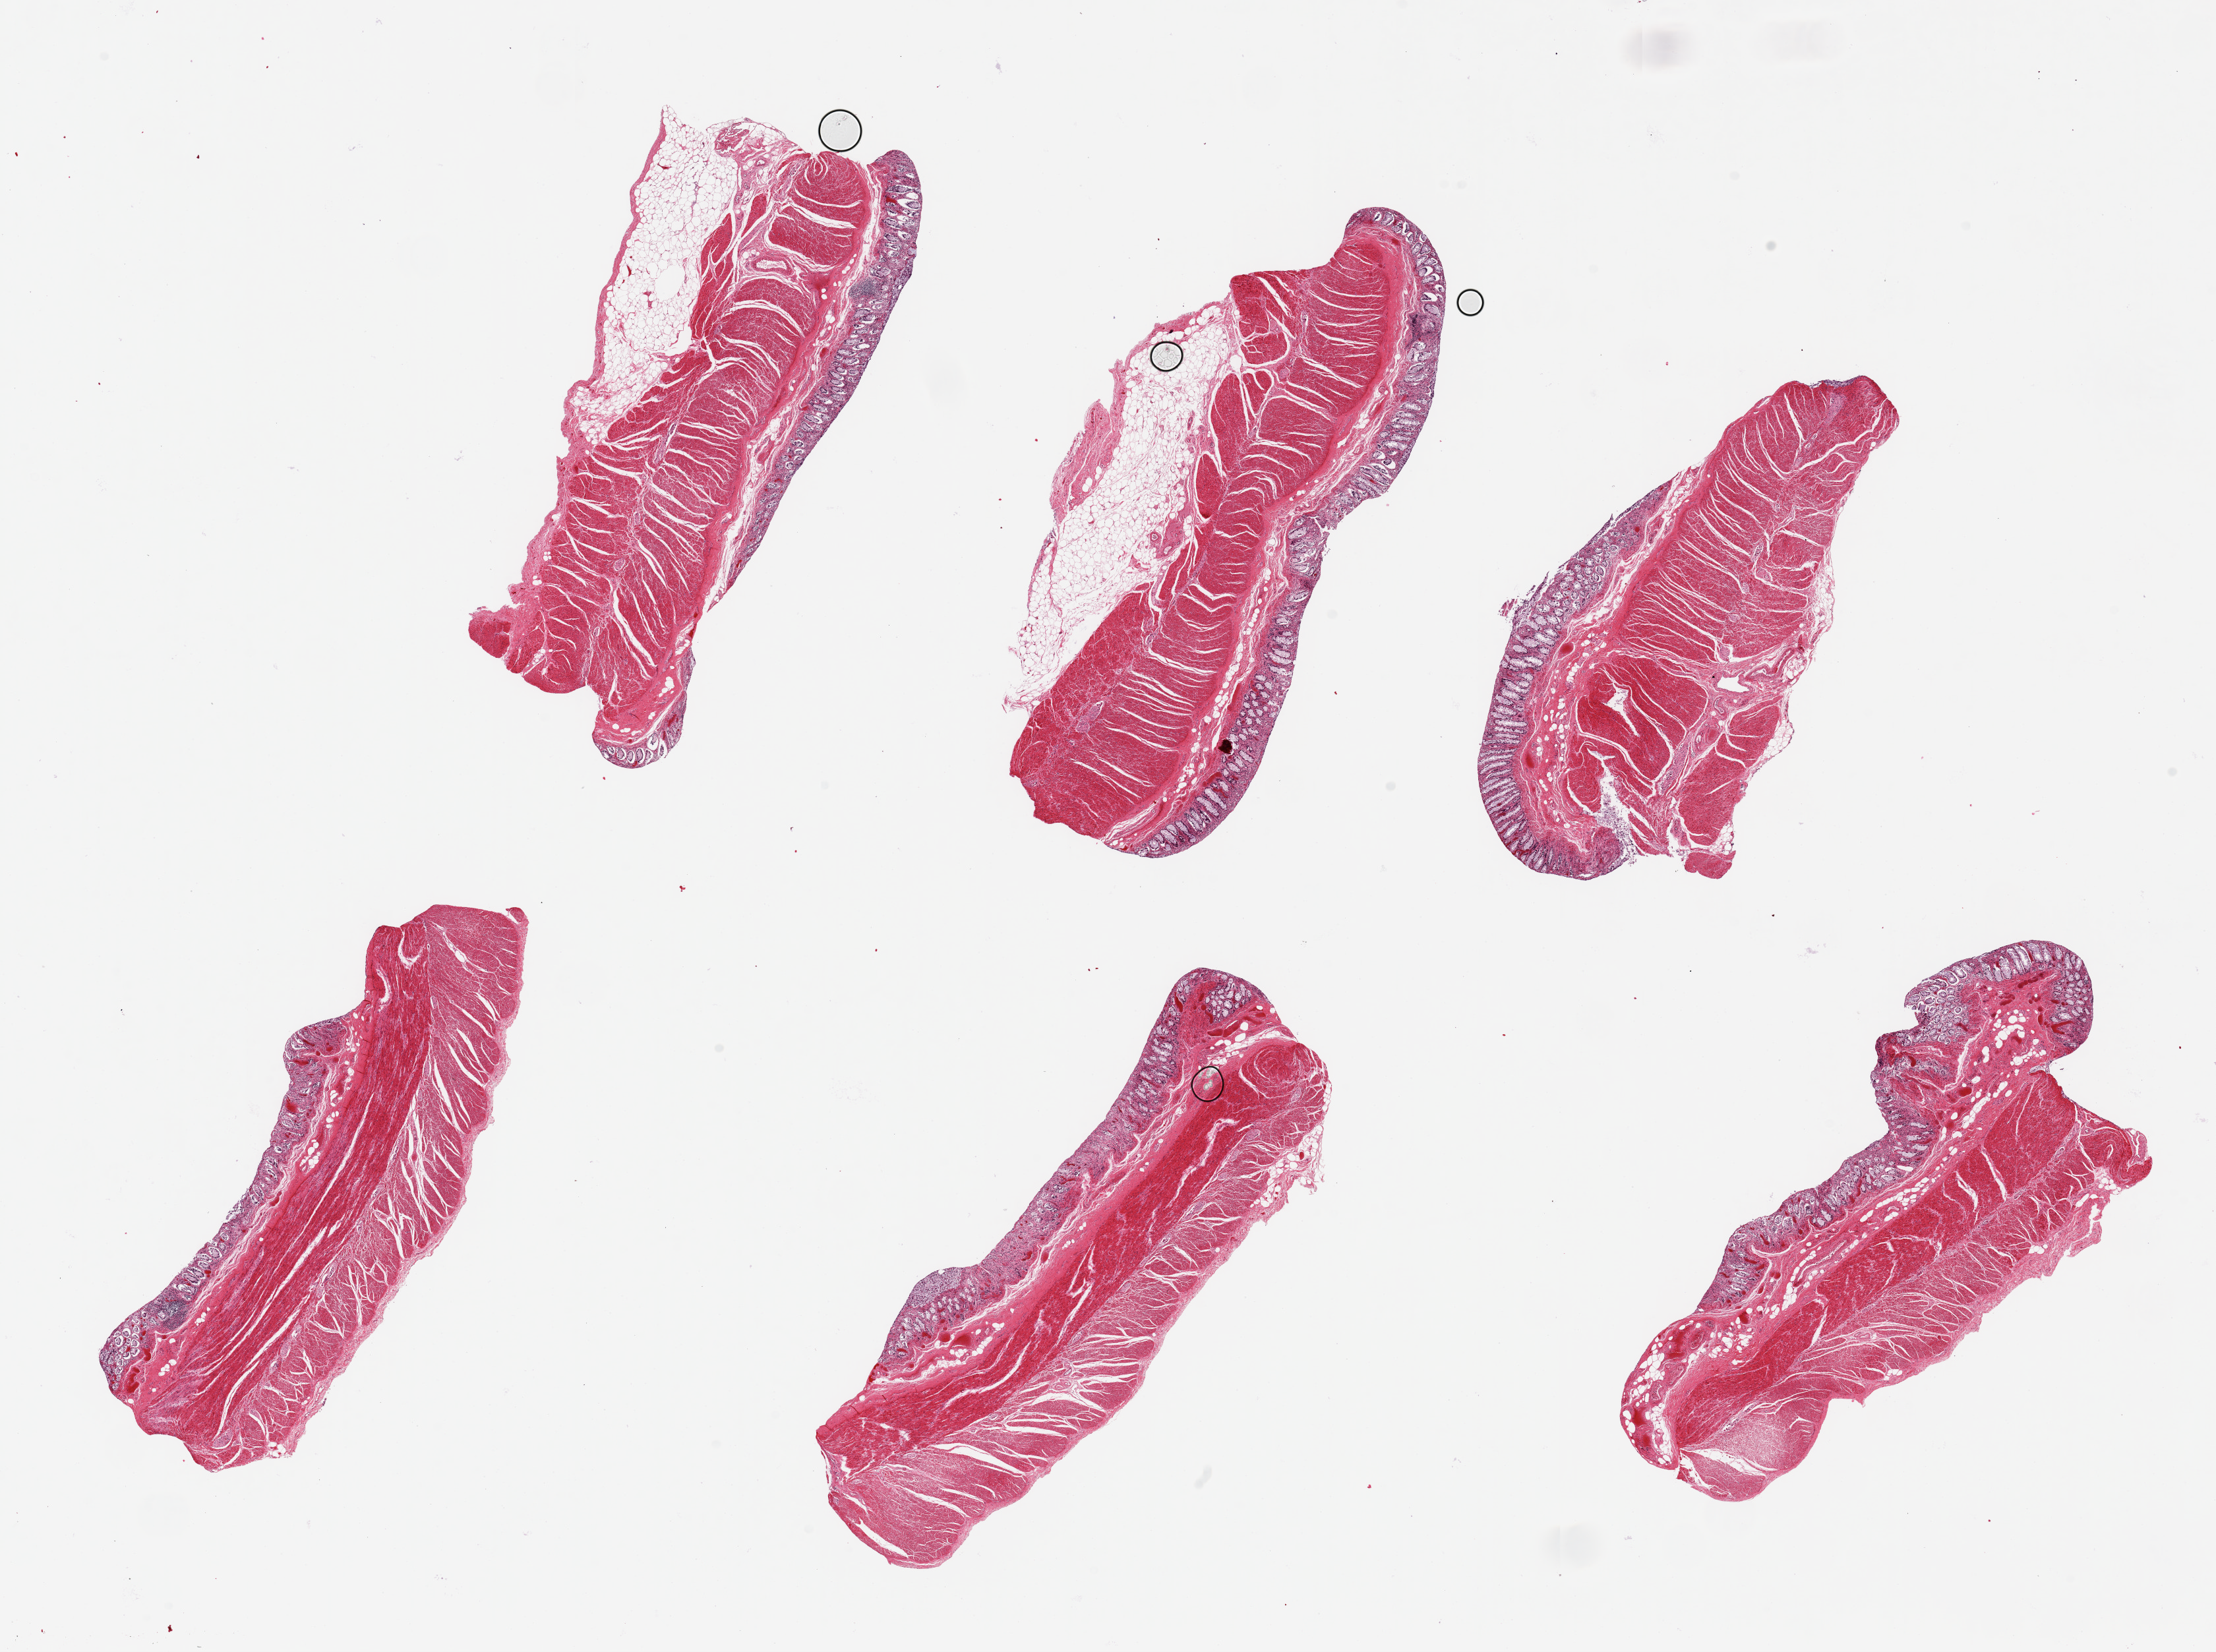
Digitized haematoxylin and eosin-stained section, brightfield — low-resolution overview of the scanned area, about 26.6 x 19.8 mm; PAXgene-fixed, paraffin-embedded tissue; sampled site (target tissue): sigmoid colon; tissue donor sample.
Review note (as recorded): 6 pieces, up to 8x4mm; all have full thickness (muscle target, mucosa not wanted).